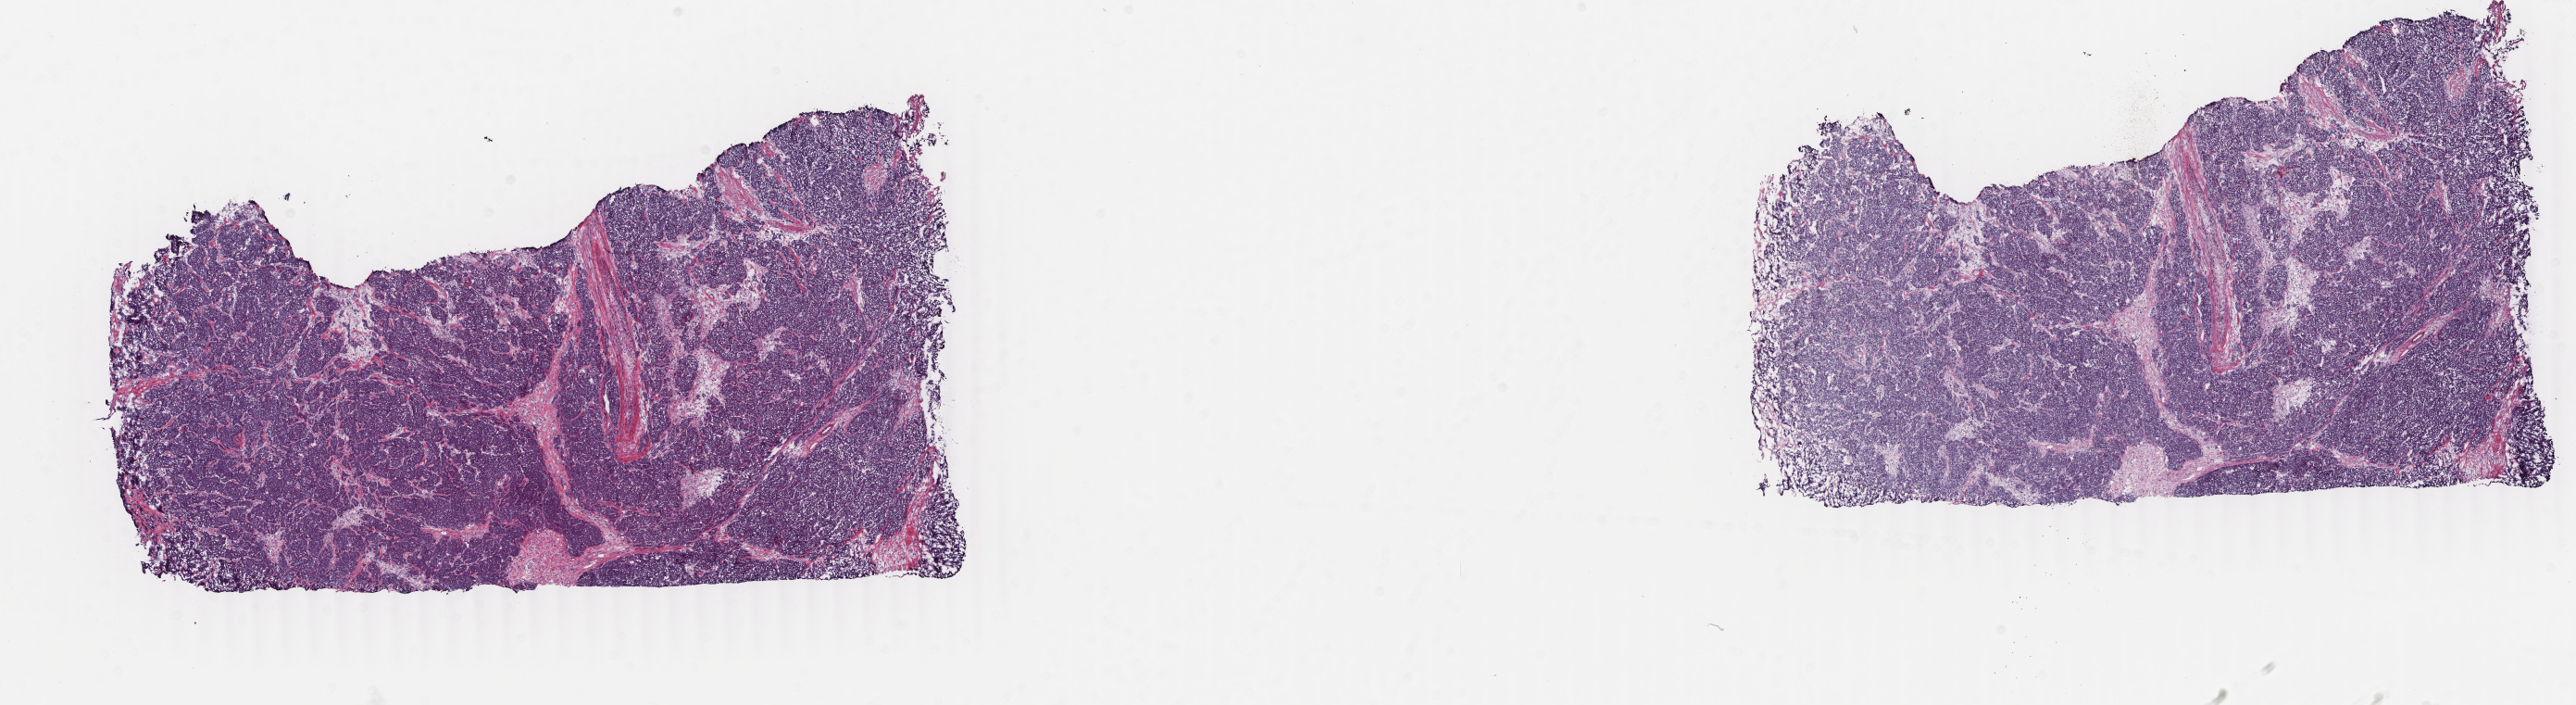
Whole-slide histology image, Hematoxylin and eosin (H&E) stained, low-resolution overview of the scanned area, about 22.1 x 6.1 mm (acquisition: 40x scan); frozen section from the bottom of the tissue portion; breast, primary tumour sample. Female patient; age at initial diagnosis 52 years. Composition of this section per pathologist review: tumour cells 88%, tumour nuclei 95%, normal cells 0%, stromal cells 10%, necrosis 2%. Inflammatory infiltration, as recorded: lymphocyte infiltration 0%, monocyte infiltration 0%, neutrophil infiltration 0%.
AJCC pathologic stage: IA. Diagnosis: Infiltrating duct carcinoma, NOS. Lymph nodes positive (case pathology): 0 of 6 examined.